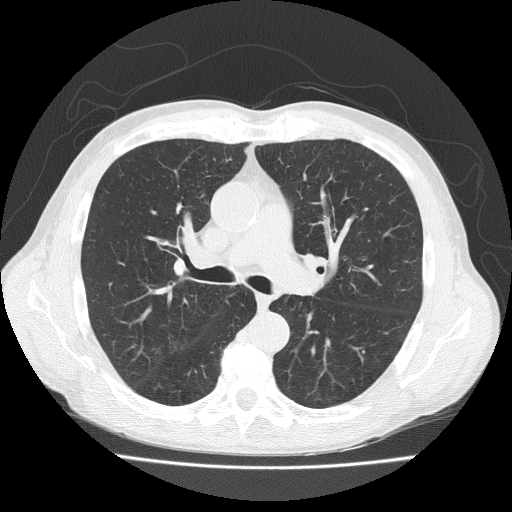
Axial slice from a low-dose chest CT screening exam, first (baseline) screen, lung window (W 1500 / L -600 HU), lung (sharp) reconstruction kernel (FC51), 512 × 512 image matrix, field of view 370 × 370 mm. Male, age 73 years at enrolment. Current smoker at enrolment.
Lesion marked by an expert reader, bounding box <143,325,190,372> (left, top, right, bottom; pixels). Screening reader's record for this exam: no non-calcified nodule ≥4 mm recorded. Official screen result: negative screen, no significant abnormalities. Later outcome: lung cancer diagnosed 777 days after this screen — adenosquamous carcinoma, right upper lobe, well differentiated (G1), stage IA (AJCC 6th edition), 20 mm at pathology.